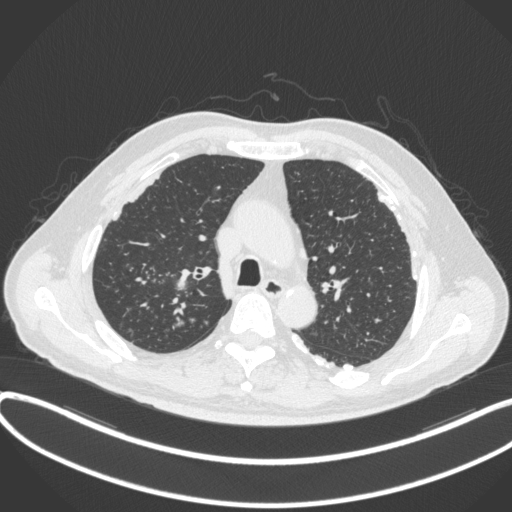
Chest CT, one axial slice; position 298 of 455 along the scan axis; 120 kVp; lung window (W 1500 / L -600 HU); 512 × 512 image matrix, field of view 400 × 400 mm. Patient: male, 58 years. Case-level facts recorded for this patient, not image findings: clinical TNM (as recorded): T1c N0 M0.
Annotated regions visible in this slice (rectangle marked by the reading radiologist):
- lung tumour (recorded histology: squamous cell carcinoma): bounding box <162,262,198,297> (left, top, right, bottom; pixels)